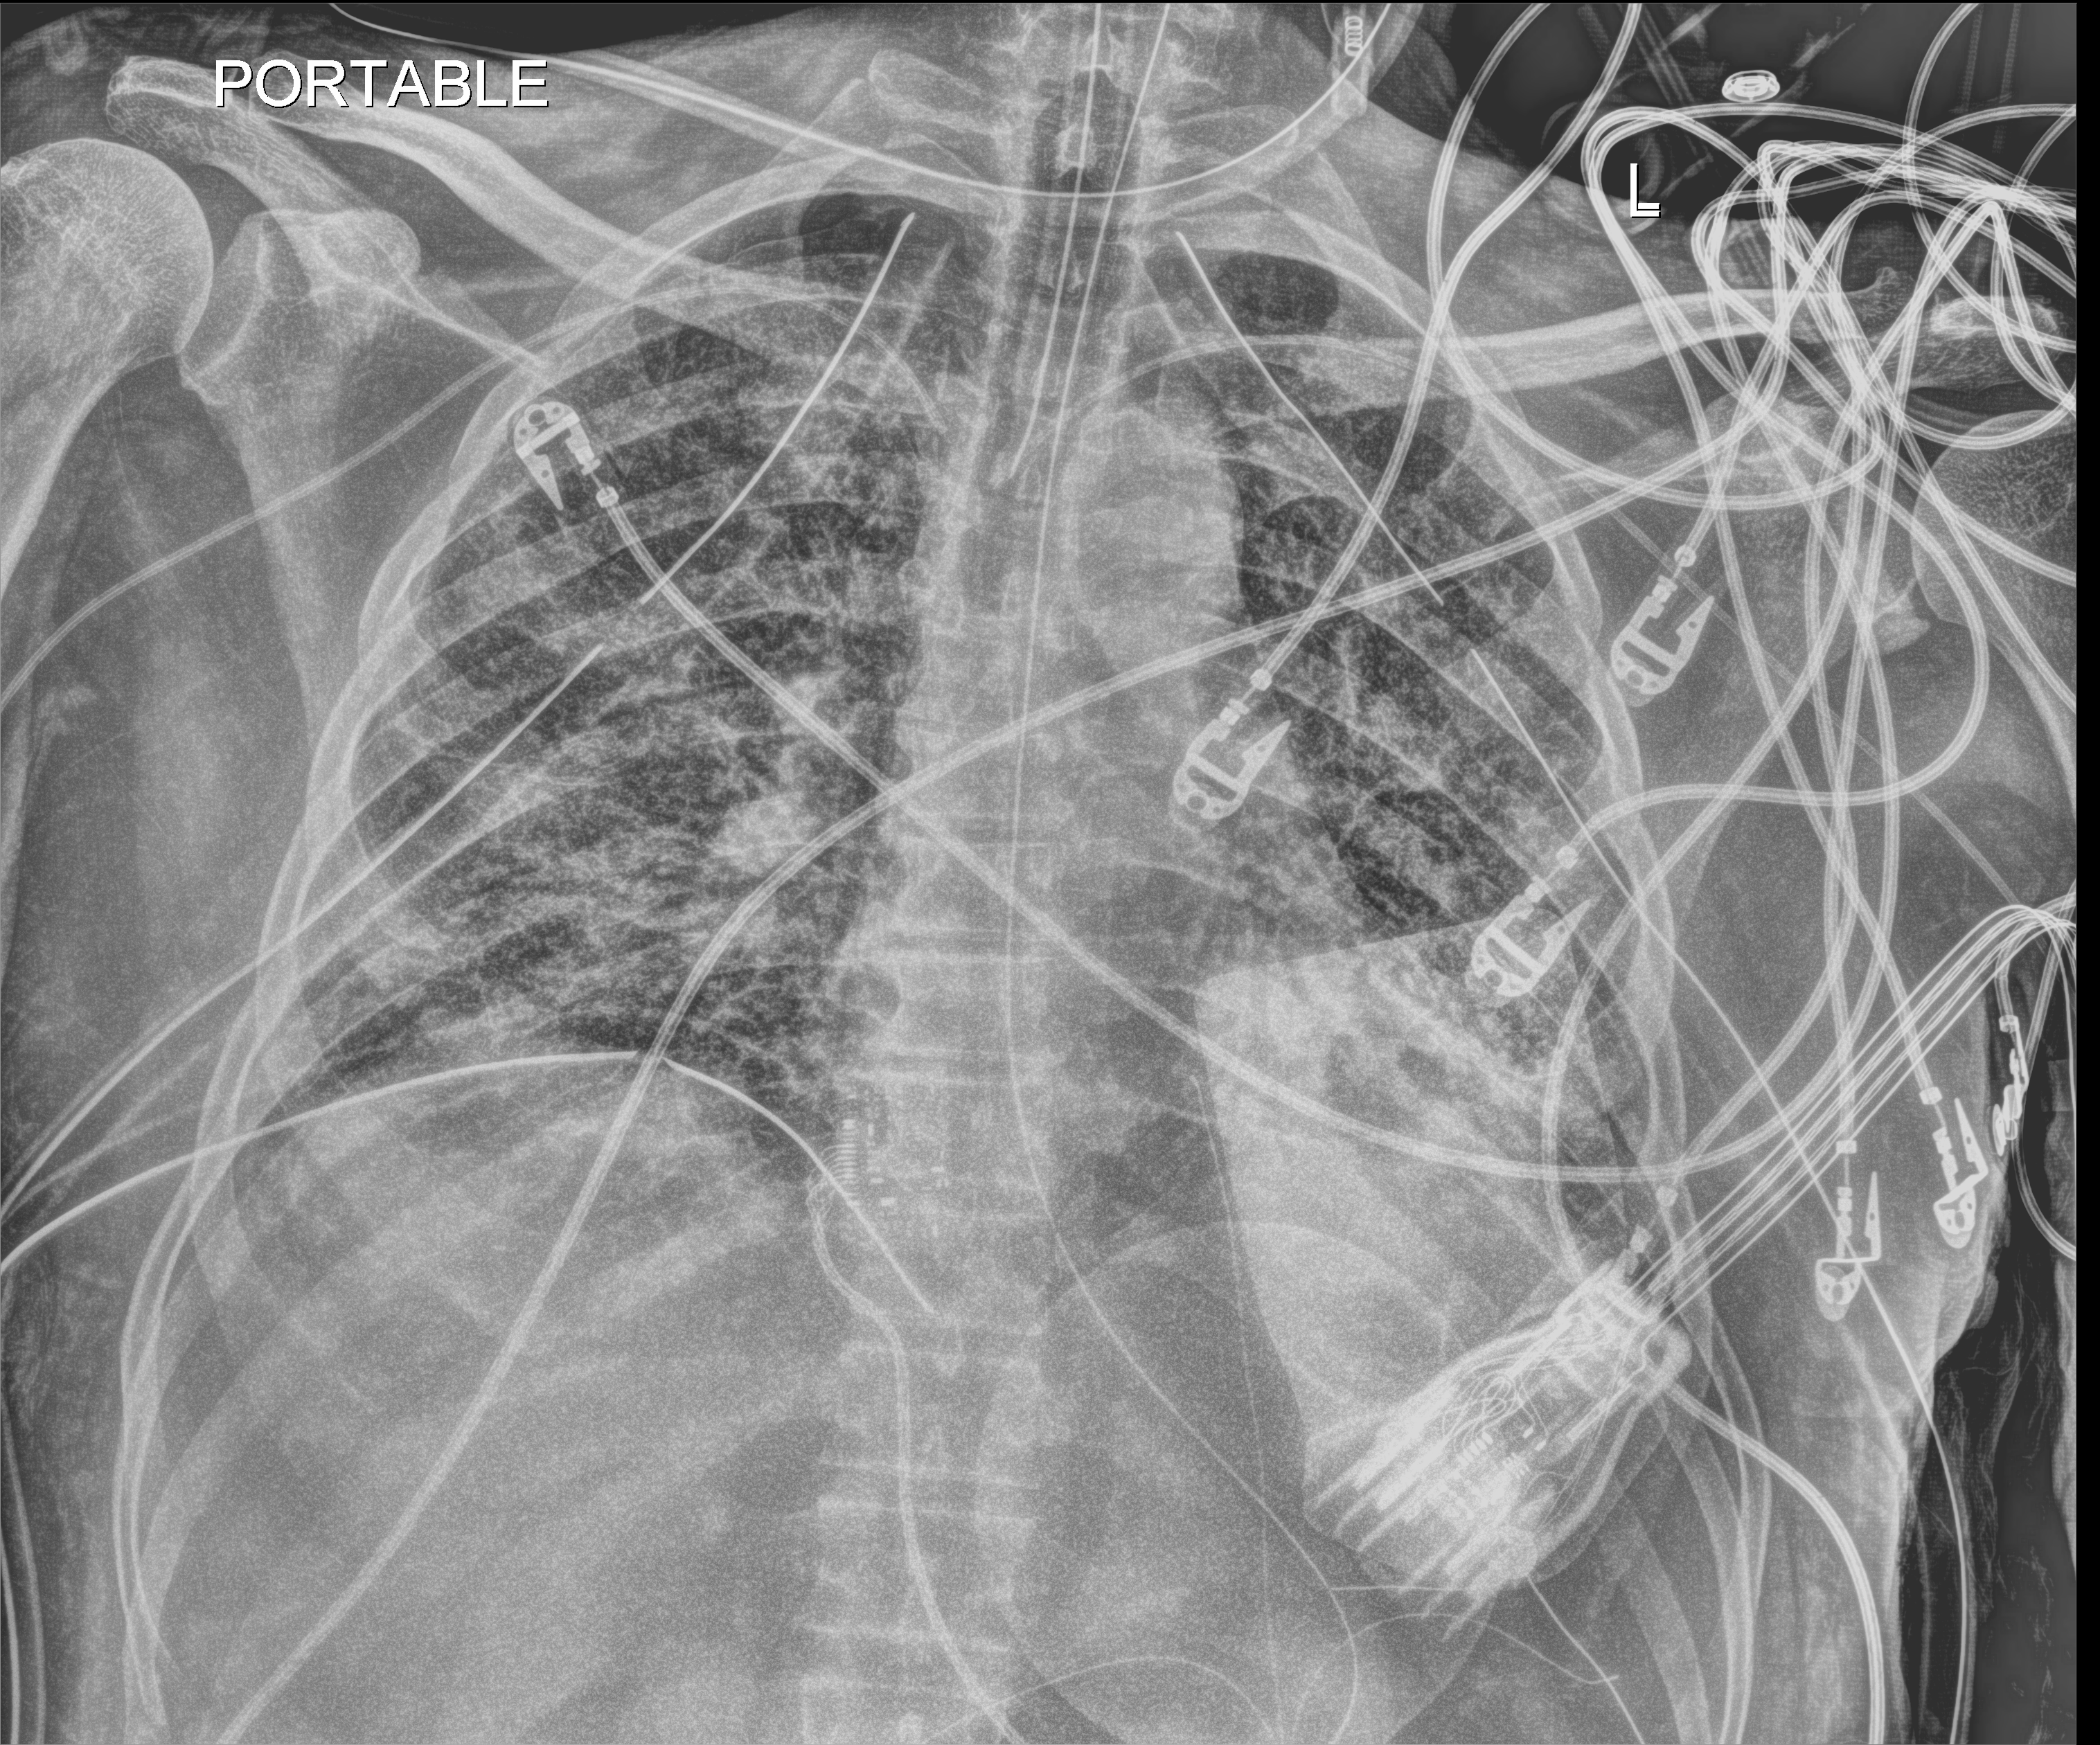
Bedside chest radiograph (digital radiography); anteroposterior (AP) projection. Patient hospitalised with COVID-19; male, aged 18–59 years.
Hospital-stay facts (about this admission, not read from this image; timing relative to this image not recorded): mechanically ventilated during this hospital stay: yes.